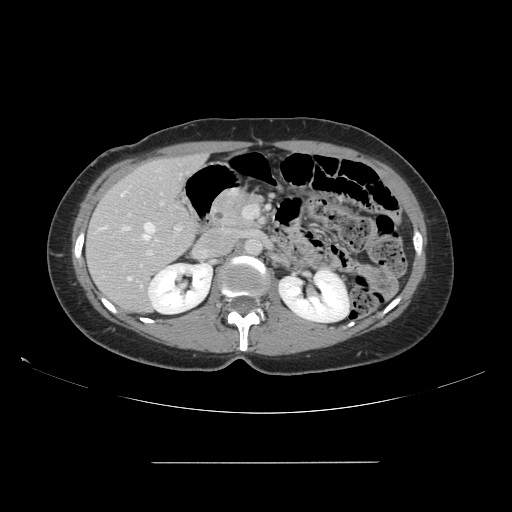
Contrast-enhanced abdominal CT, one axial slice; position 82 of 151 along the scan axis; intravenous contrast given; soft-tissue window (W 400 / L 40 HU); 512 × 512 image matrix, field of view 421 × 421 mm. Female patient, age 46 years. From the clinical record (not read from this slice): diagnosis: colorectal cancer liver metastases, imaged before liver resection; multiple liver metastases: yes; largest metastasis: 3 cm; chemotherapy before resection: no.
Outlined on this slice (manually delineated by an expert):
- hepatic veins: bounding box (x1, y1, x2, y2) in pixels: (120, 190, 156, 279)
- liver: (87, 155, 206, 313)
- planned liver remnant (the part of the liver to remain after resection): (96, 156, 201, 313)
- portal vein (with intrahepatic branches): (128, 192, 247, 260)